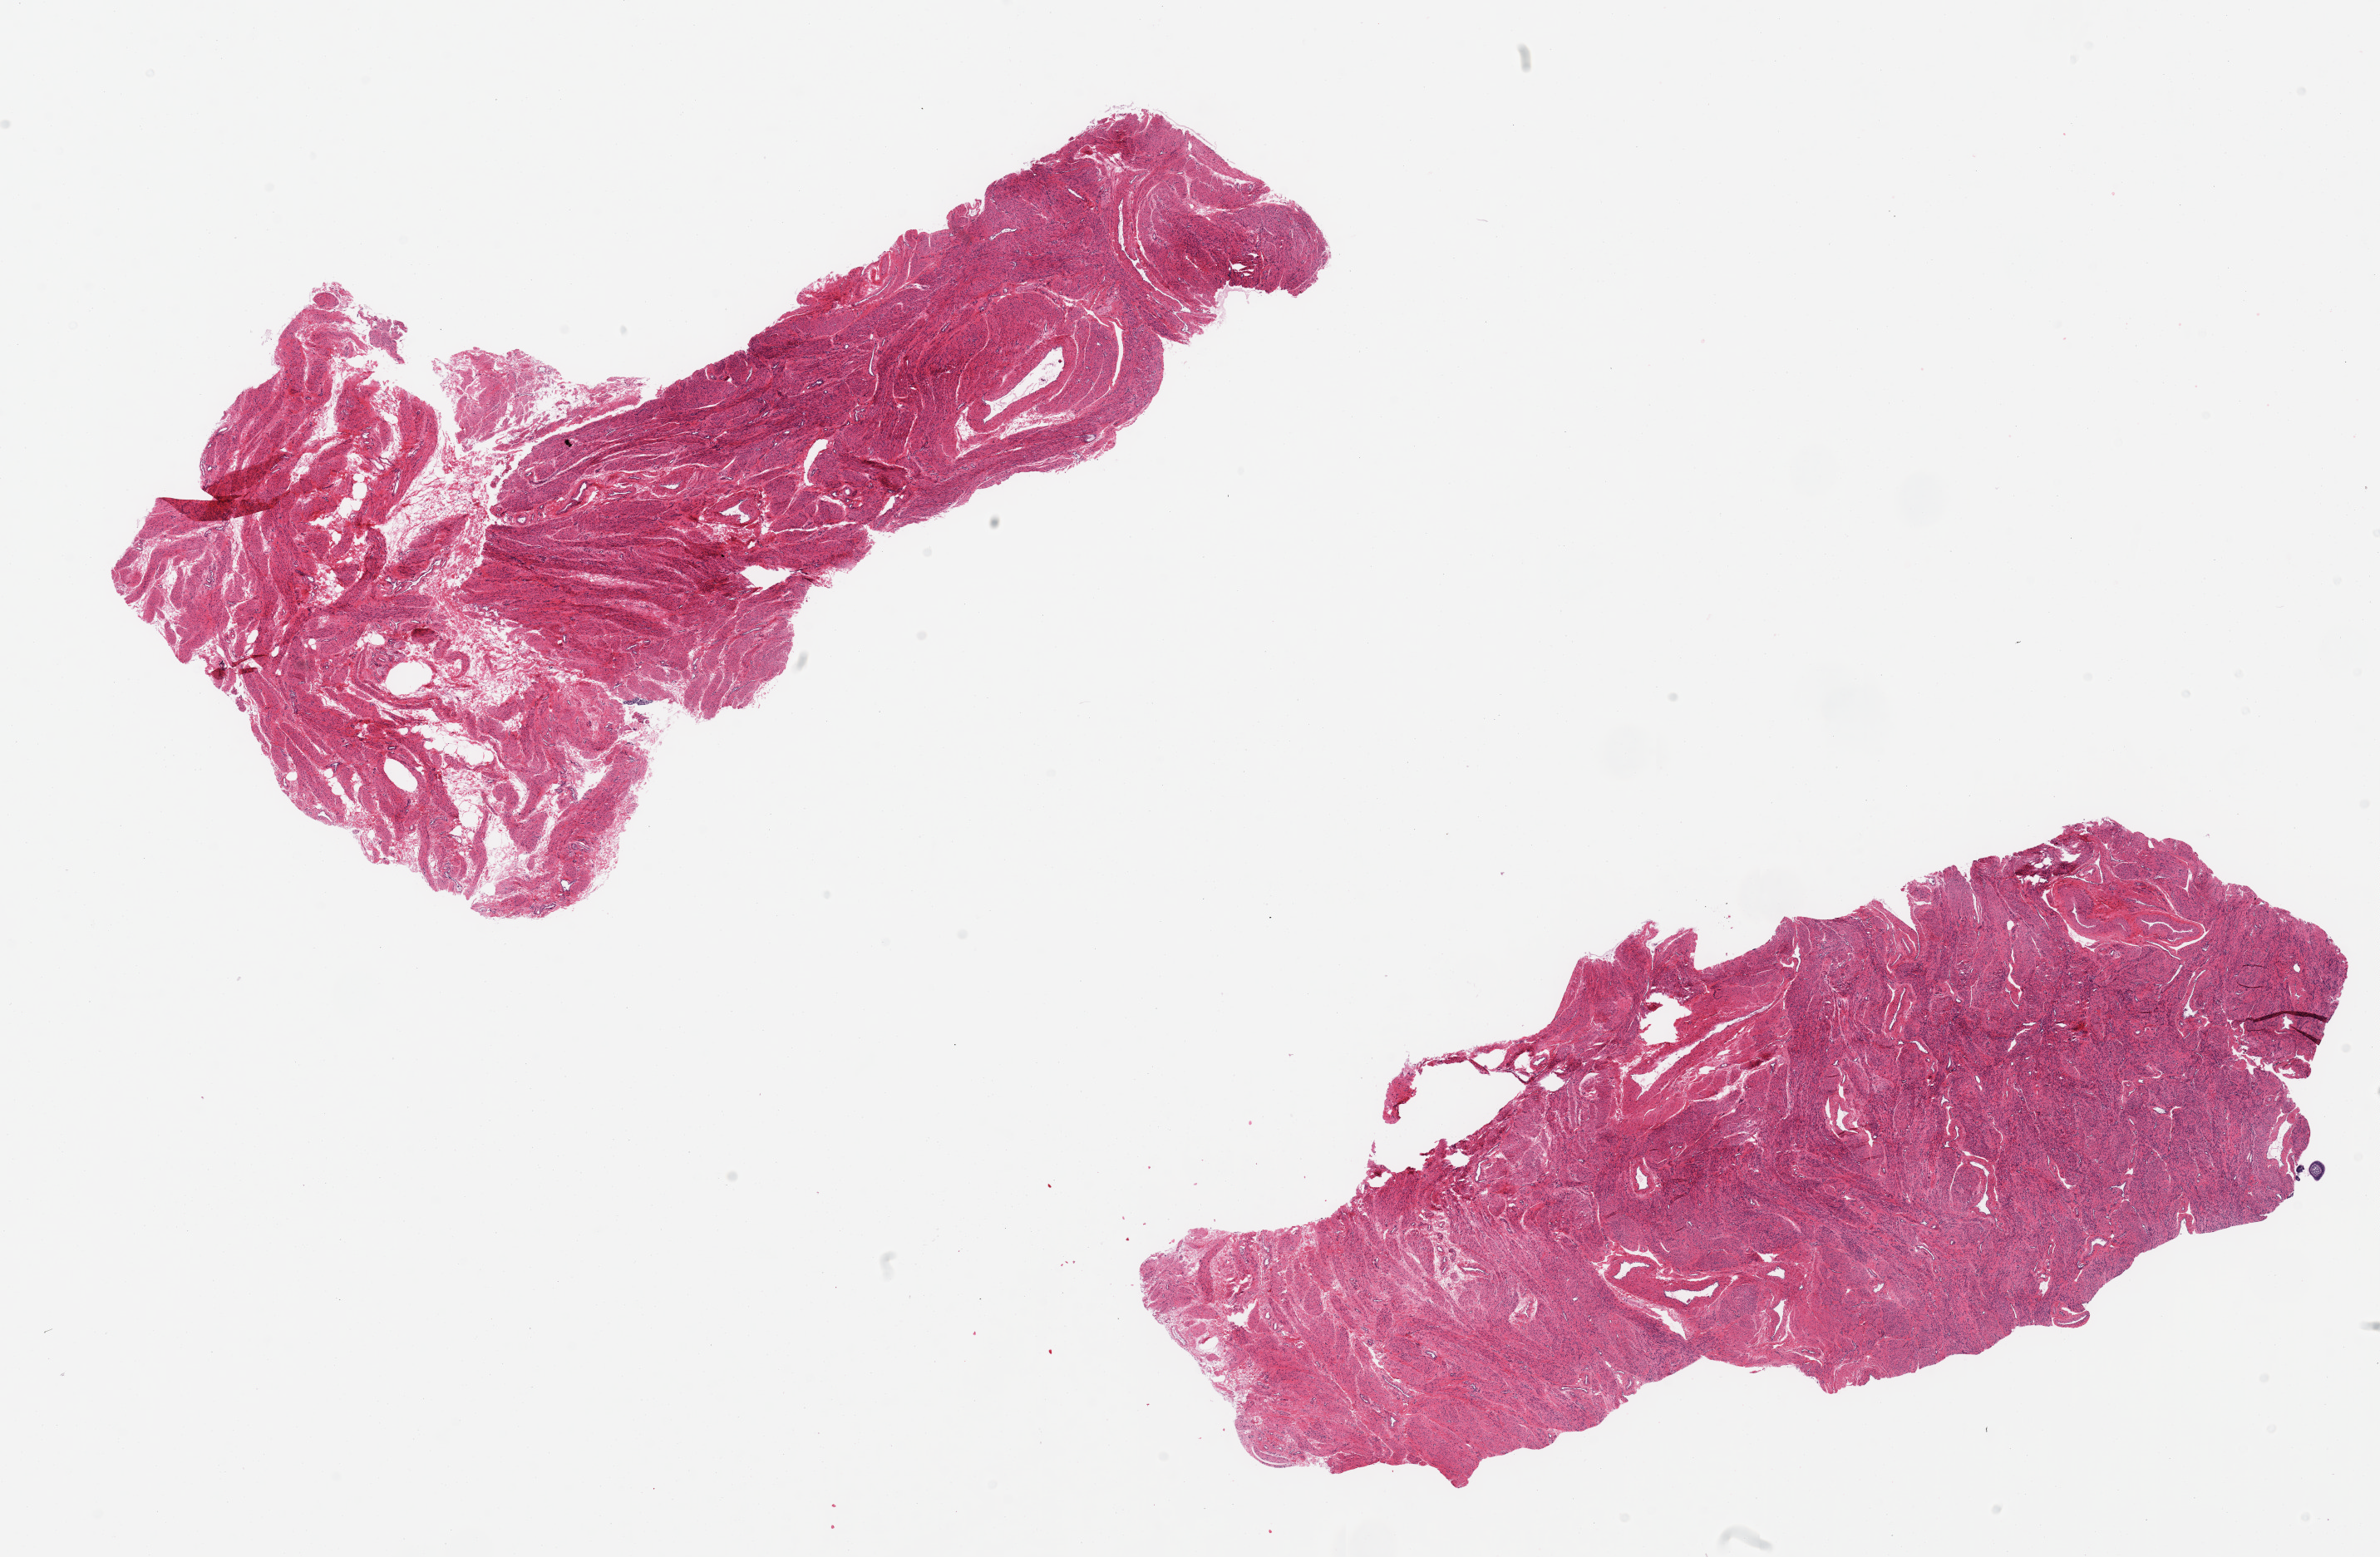
Haematoxylin and eosin whole-slide image — a low-resolution overview of the entire scanned area, about 22.6 x 14.8 mm; PAXgene-fixed paraffin-embedded (PFPE) section; sampled site (target tissue): uterus; tissue donor sample. Donor sex: female.
Pathologist's review note for this sample: 2 pieces, myometrium only.